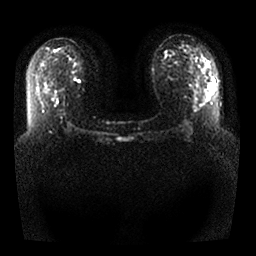
Breast MRI, one axial slice; slice 17 of 25 in the series (ordered by position); diffusion-weighted series; image 2 of 4 stored at this slice position (different b-values; order by instance number); 1.5 T; 256 × 256 image matrix, field of view 340 × 340 mm. Female patient.
Annotated regions visible in this slice (manually delineated by an expert):
- tumour on diffusion-weighted imaging: bounding box [x1, y1, x2, y2] px = [211, 79, 213, 84]